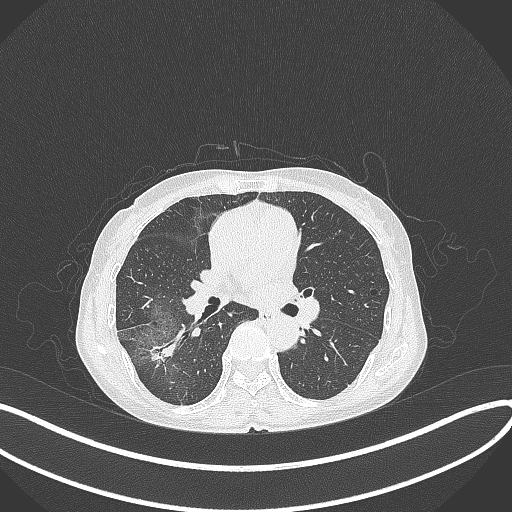
Chest CT, one axial slice; slice 214 of 371 in the series (ordered by position); lung window (W 1500 / L -600 HU); 512 × 512 image matrix. Patient: female, 69 years. From the clinical record (not read from this slice): clinical TNM (as recorded): T1b N0 M0.
Outlined on this slice (bounding box drawn by a radiologist):
- lung tumour (recorded histology: adenocarcinoma): bounding box <143,332,182,368> (left, top, right, bottom; pixels)